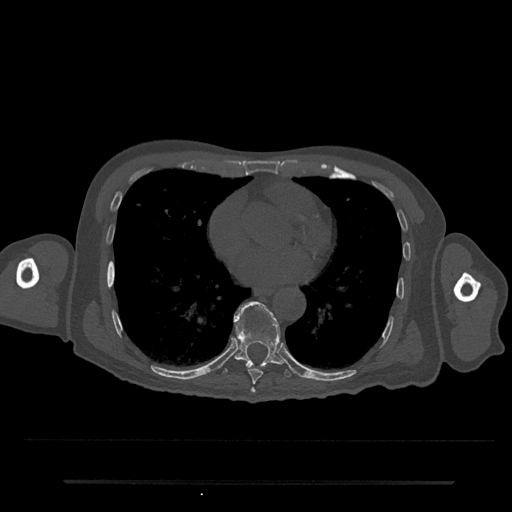
CT including the spine, one axial slice. 120 kVp. Bone window (W 1800 / L 400 HU). 512 × 512 image matrix, field of view 427 × 427 mm. Patient: male, 74 years. From the clinical record (not read from this slice): primary cancer: prostate.
Annotated regions visible in this slice (semi-automatically segmented with operator editing):
- T7 vertebra: bounding box (x1, y1, x2, y2) in pixels: (250, 388, 256, 394)
- T8 vertebra: (248, 369, 263, 385)
- T9 vertebra: (223, 301, 291, 379)